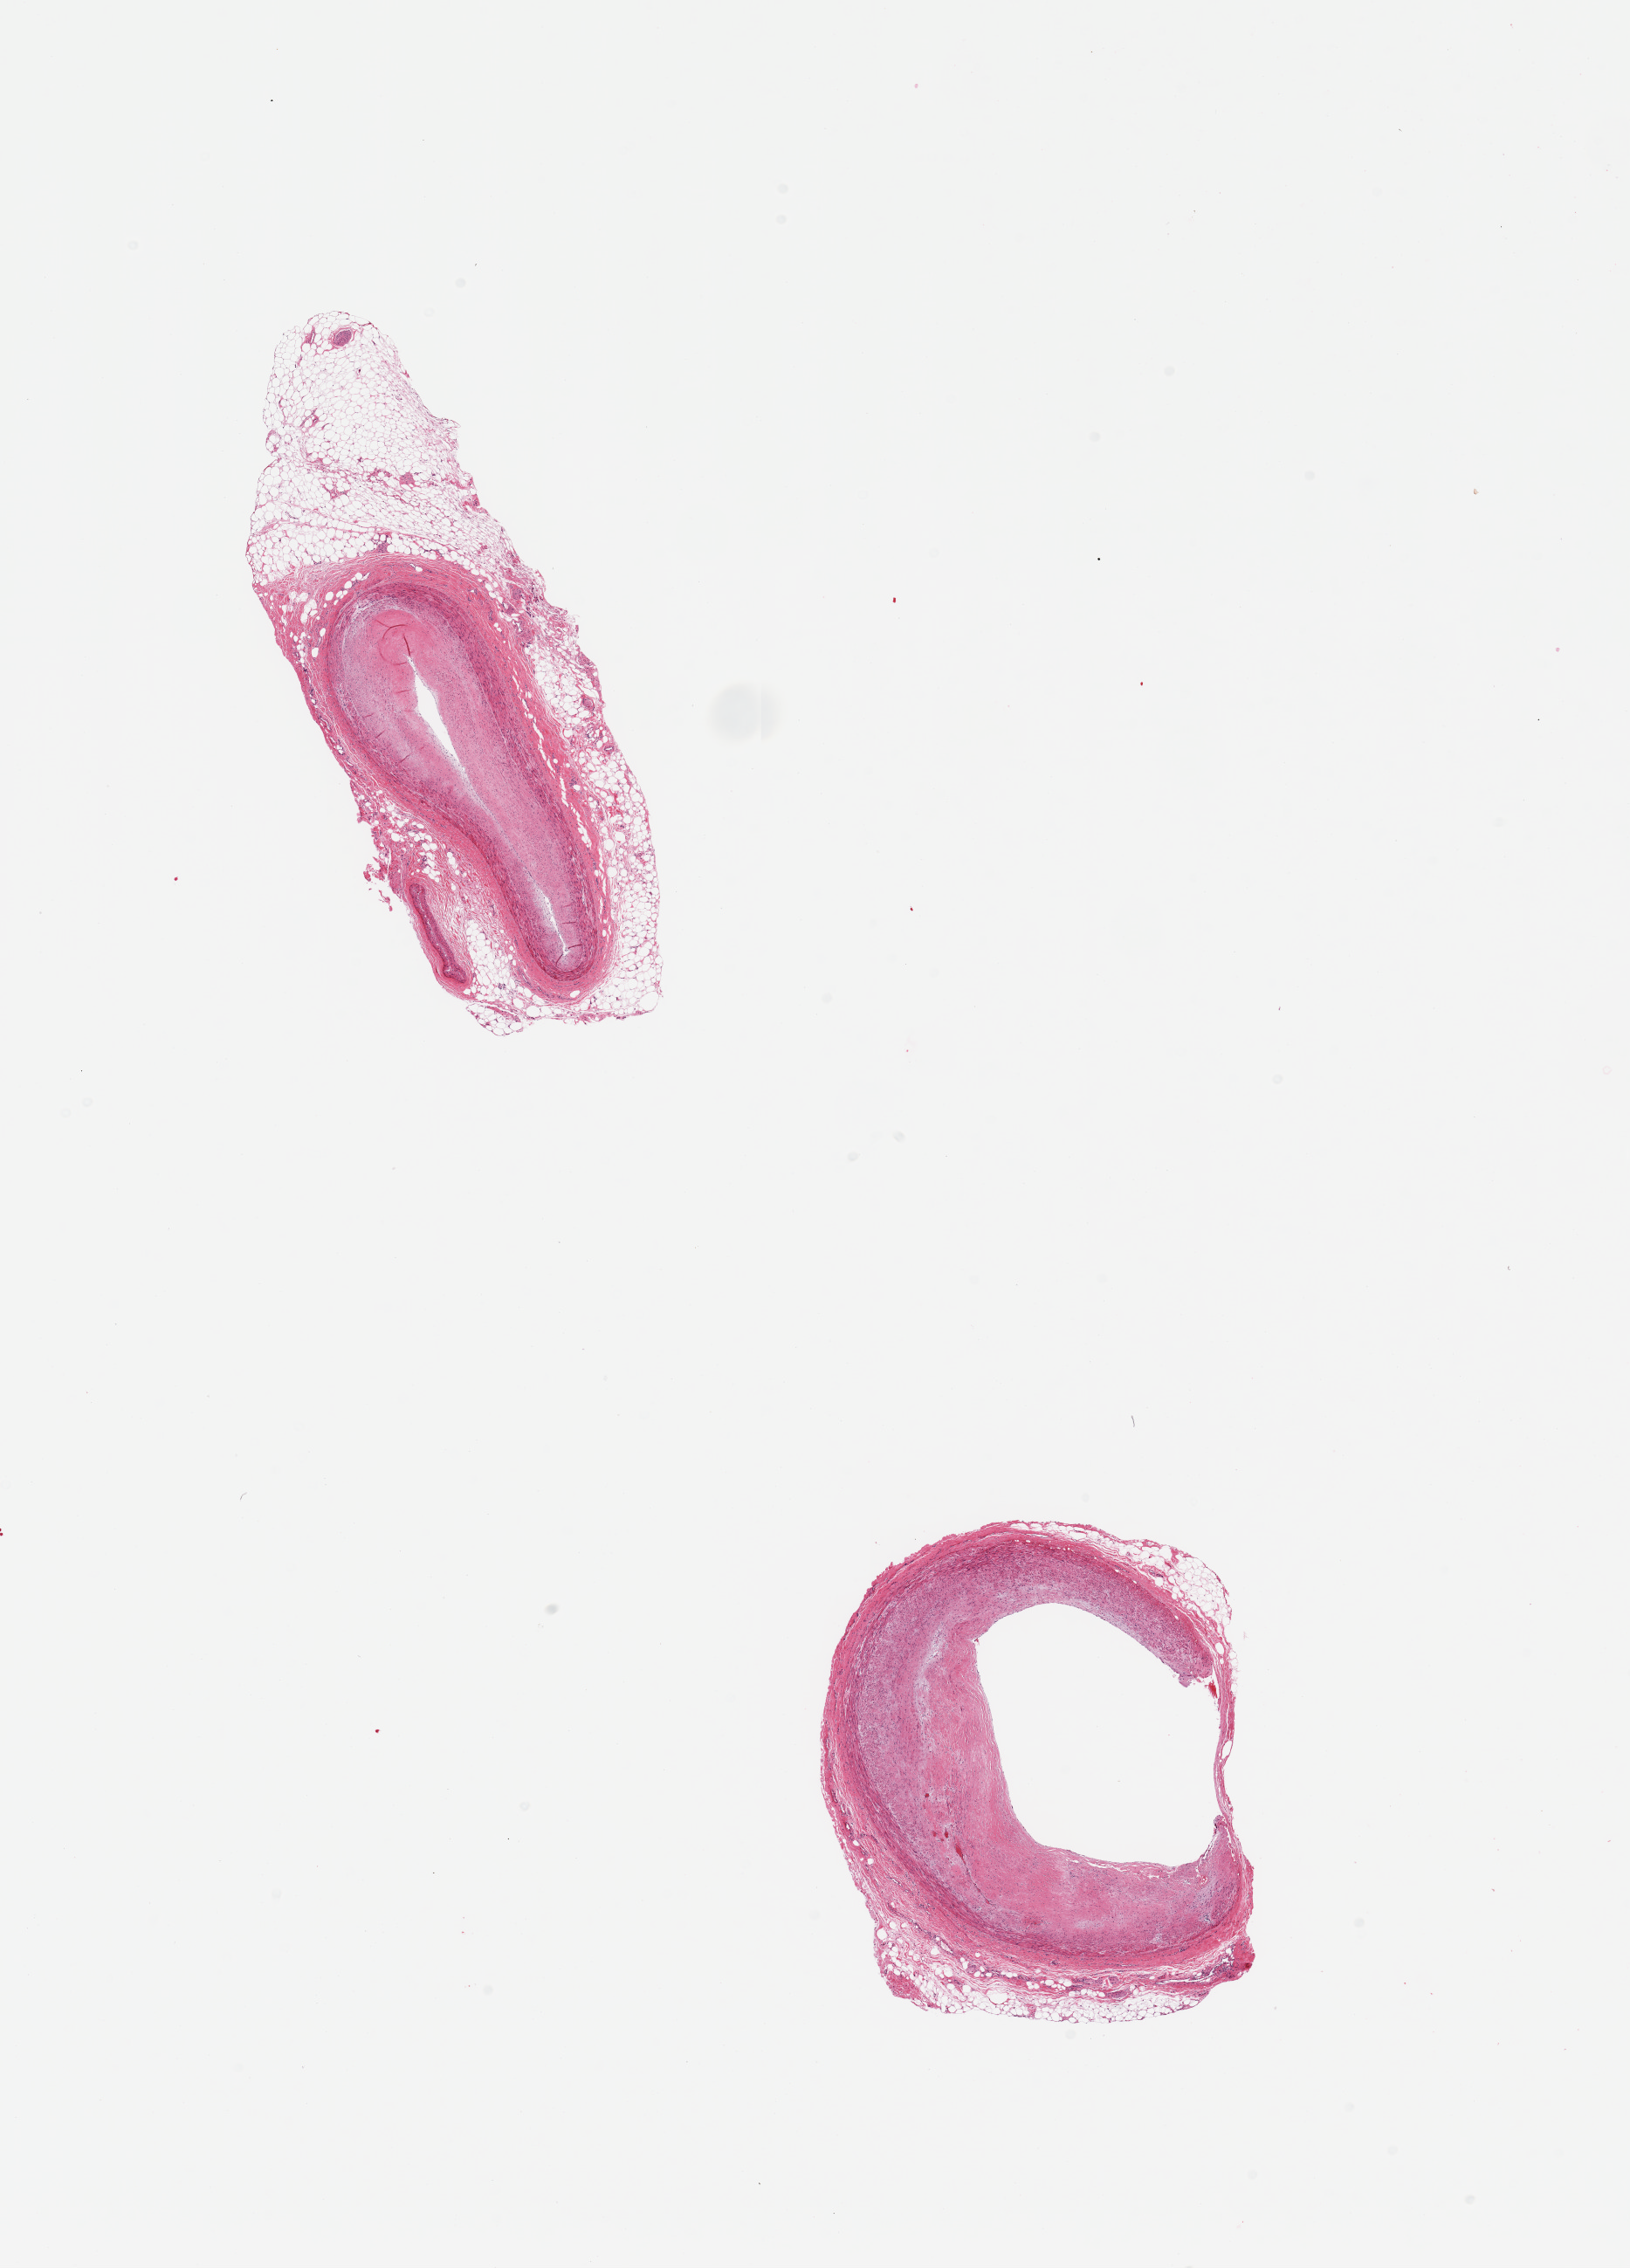
Whole-slide image, hematoxylin and eosin (H&E) stain, whole scanned area (about 14.8 x 20.5 mm) shown as a low-resolution overview; PAXgene-fixed paraffin-embedded (PFPE) section; target tissue: coronary artery; tissue donor sample. Donor: male.
• reviewer comment on this tissue sample: 2 pieces; ~1mm eccentric fibrosclerotic plaque narrowing the lumen by 50%; up to 2mm adventitial fat